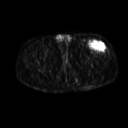
FDG PET of an extremity soft-tissue mass (from a PET/CT study), one axial slice; slice 253 of 267 in the series (ordered by position); 3.27 mm slice thickness; 128 × 128 image matrix. Patient: male, 64 years. From the clinical record (not read from this slice): histological type: extraskeletal osteosarcoma; grade: high; site of the primary tumour: thigh.
Structures marked on this image (expert contour drawn on MRI and transferred to this co-registered scan by the dataset authors):
- gross tumour volume (mass): box from (x=90, y=42) to (x=105, y=50) px